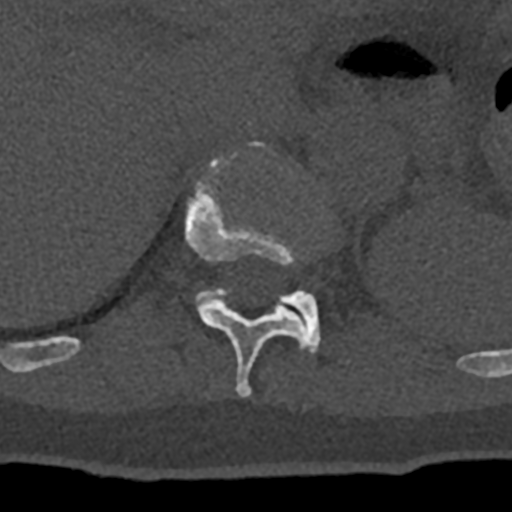
CT including the spine, one axial slice; position 531 of 797 along the scan axis; 120 kVp; bone window (W 1800 / L 400 HU); 0.5 mm slice thickness; 512 × 512 image matrix, field of view 160 × 160 mm. Patient: male, 74 years. From the clinical record (not read from this slice): primary cancer: renal.
Structures marked on this image (semi-automatically segmented with operator editing):
- T11 vertebra: bounding box [x1, y1, x2, y2] px = [70, 141, 308, 398]
- T12 vertebra: [195, 288, 321, 353]